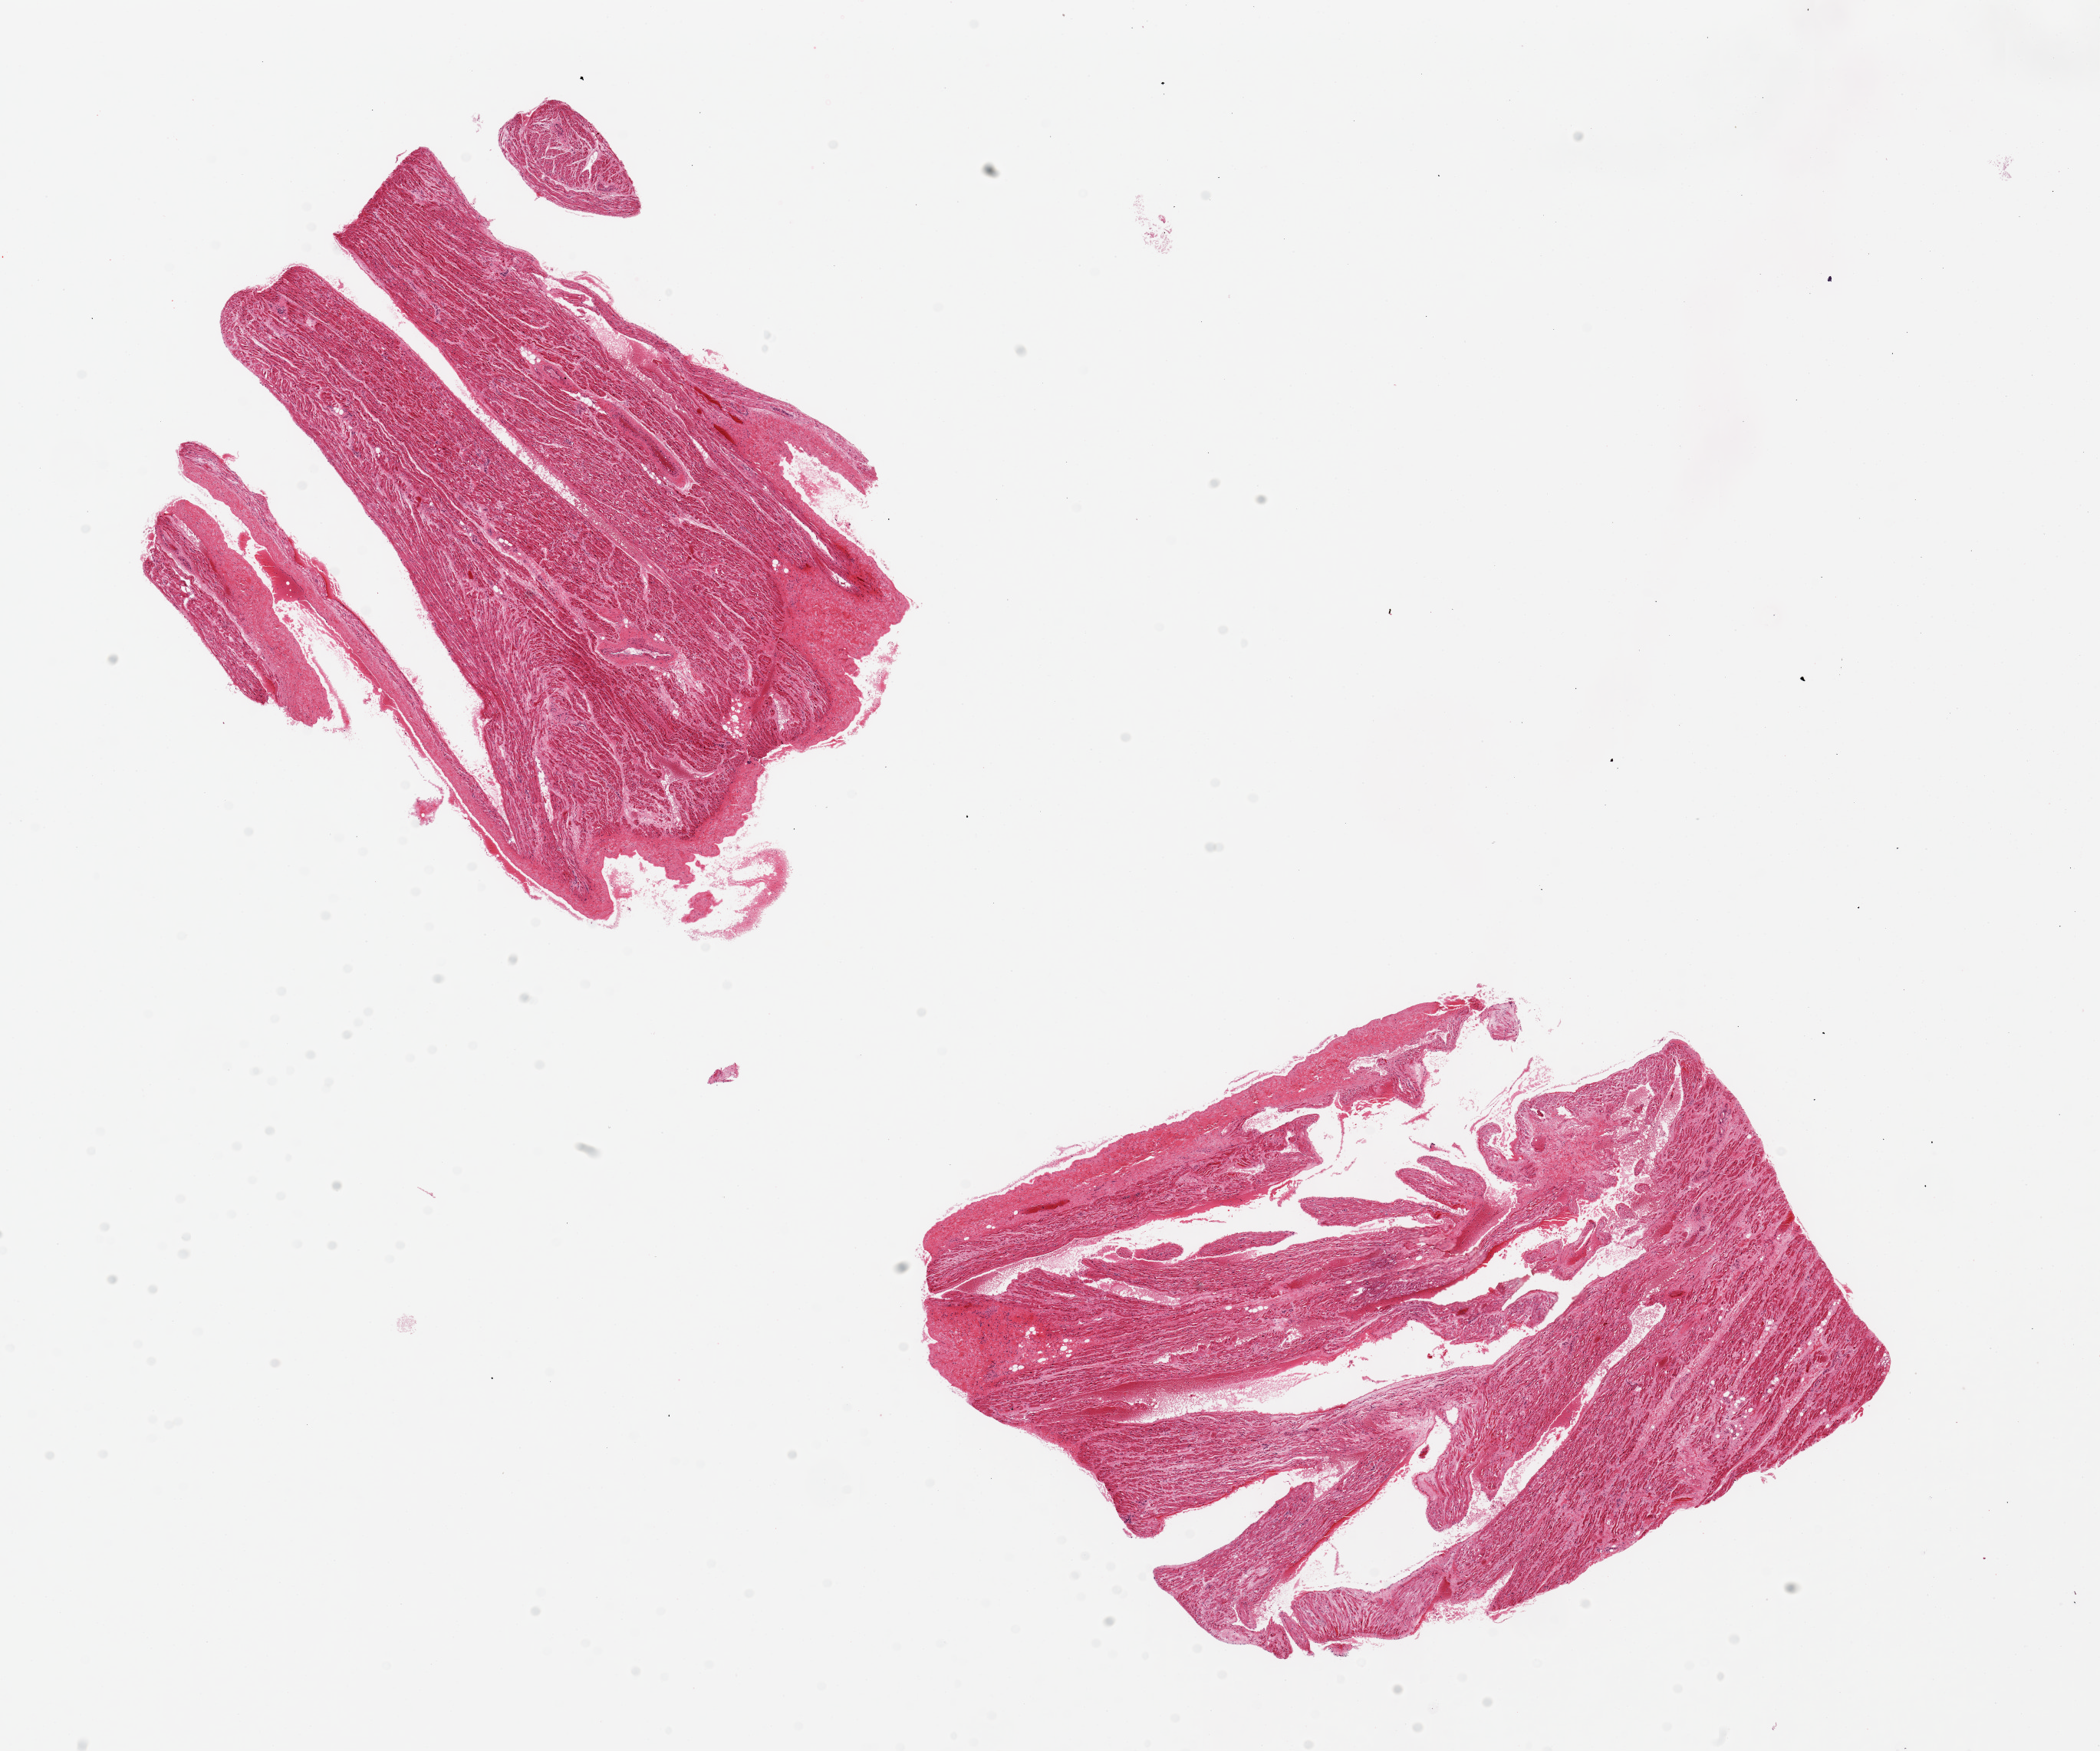
Whole-slide image, hematoxylin and eosin (H&E) stain — low-resolution overview of the scanned area, about 21.7 x 18.1 mm; PAXgene-fixed paraffin-embedded (PFPE) section; section of auricular appendage (target tissue); donor tissue sample. Donor sex: female.
Pathologist's review note for this sample: 2 pieces `7x6mm.